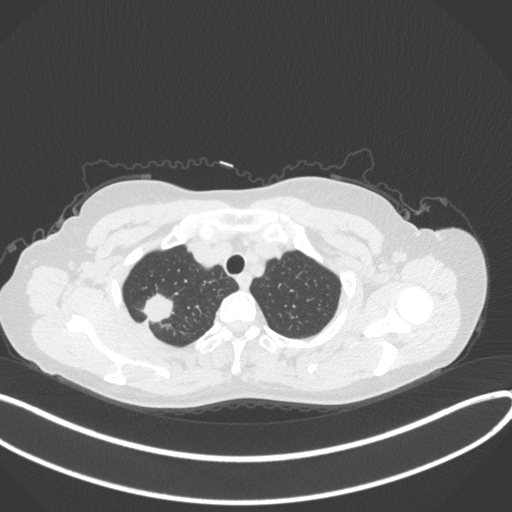
Chest CT, one axial slice. Position 315 of 342 along the scan axis. Lung window (W 1500 / L -600 HU). 512 × 512 image matrix, field of view 400 × 400 mm. Patient: female, 50 years. Case-level facts recorded for this patient, not image findings: clinical TNM (as recorded): T1c N0 M0.
Annotated regions visible in this slice (rectangle marked by the reading radiologist):
- lung tumour (recorded histology: adenocarcinoma): box from (x=141, y=290) to (x=176, y=325) px